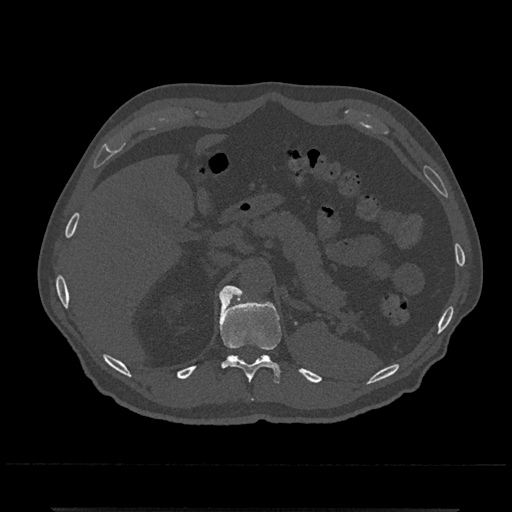
CT including the spine, one axial slice. Position 483 of 797 along the scan axis. Reconstruction kernel Br40s/3. 120 kVp. Bone window (W 1800 / L 400 HU). 0.5 mm slice thickness. 512 × 512 image matrix. Patient: male, 67 years. Case-level facts recorded for this patient, not image findings: primary cancer: prostate.
Annotated regions visible in this slice (semi-automatically segmented with operator editing):
- T11 vertebra: bounding box [x1, y1, x2, y2] px = [219, 293, 282, 401]
- T12 vertebra: [221, 285, 243, 297]